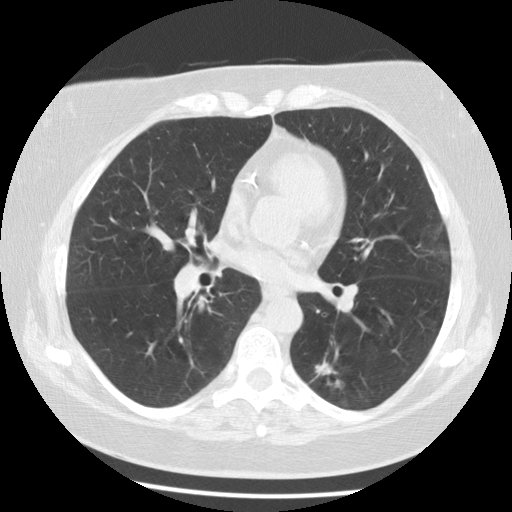
Low-dose screening chest CT, one axial slice. Slice 58 of 116 in the series (ordered by position). Reconstruction kernel STANDARD. Lung window (W 1500 / L -600 HU). 2.5 mm slice thickness. 512 × 512 image matrix, field of view 341 × 341 mm.
Structures marked on this image (manually delineated by an expert):
- lesion 1 (tumor, lower lobe of left lung): bounding box [x1, y1, x2, y2] px = [315, 362, 334, 375]